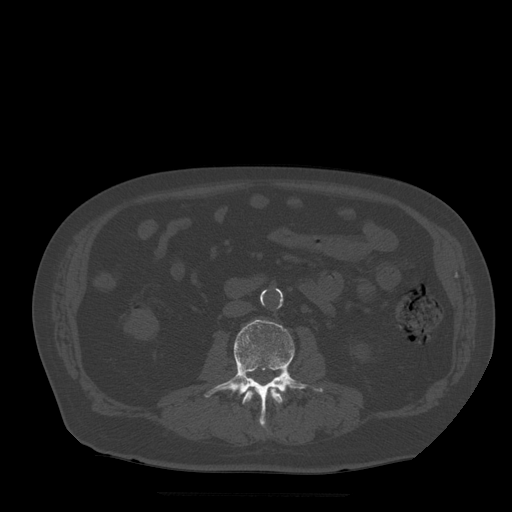
CT including the spine, one axial slice; slice 143 of 522 in the series (ordered by position); bone window (W 1800 / L 400 HU); 1.25 mm slice thickness; 512 × 512 image matrix, field of view 420 × 420 mm. Patient age 72 years. From the clinical record (not read from this slice): primary cancer: prostate.
Structures marked on this image (semi-automatic segmentation, software-assisted and operator-edited):
- L2 vertebra: bounding box [x1, y1, x2, y2] px = [243, 384, 287, 428]
- L3 vertebra: [204, 320, 324, 425]